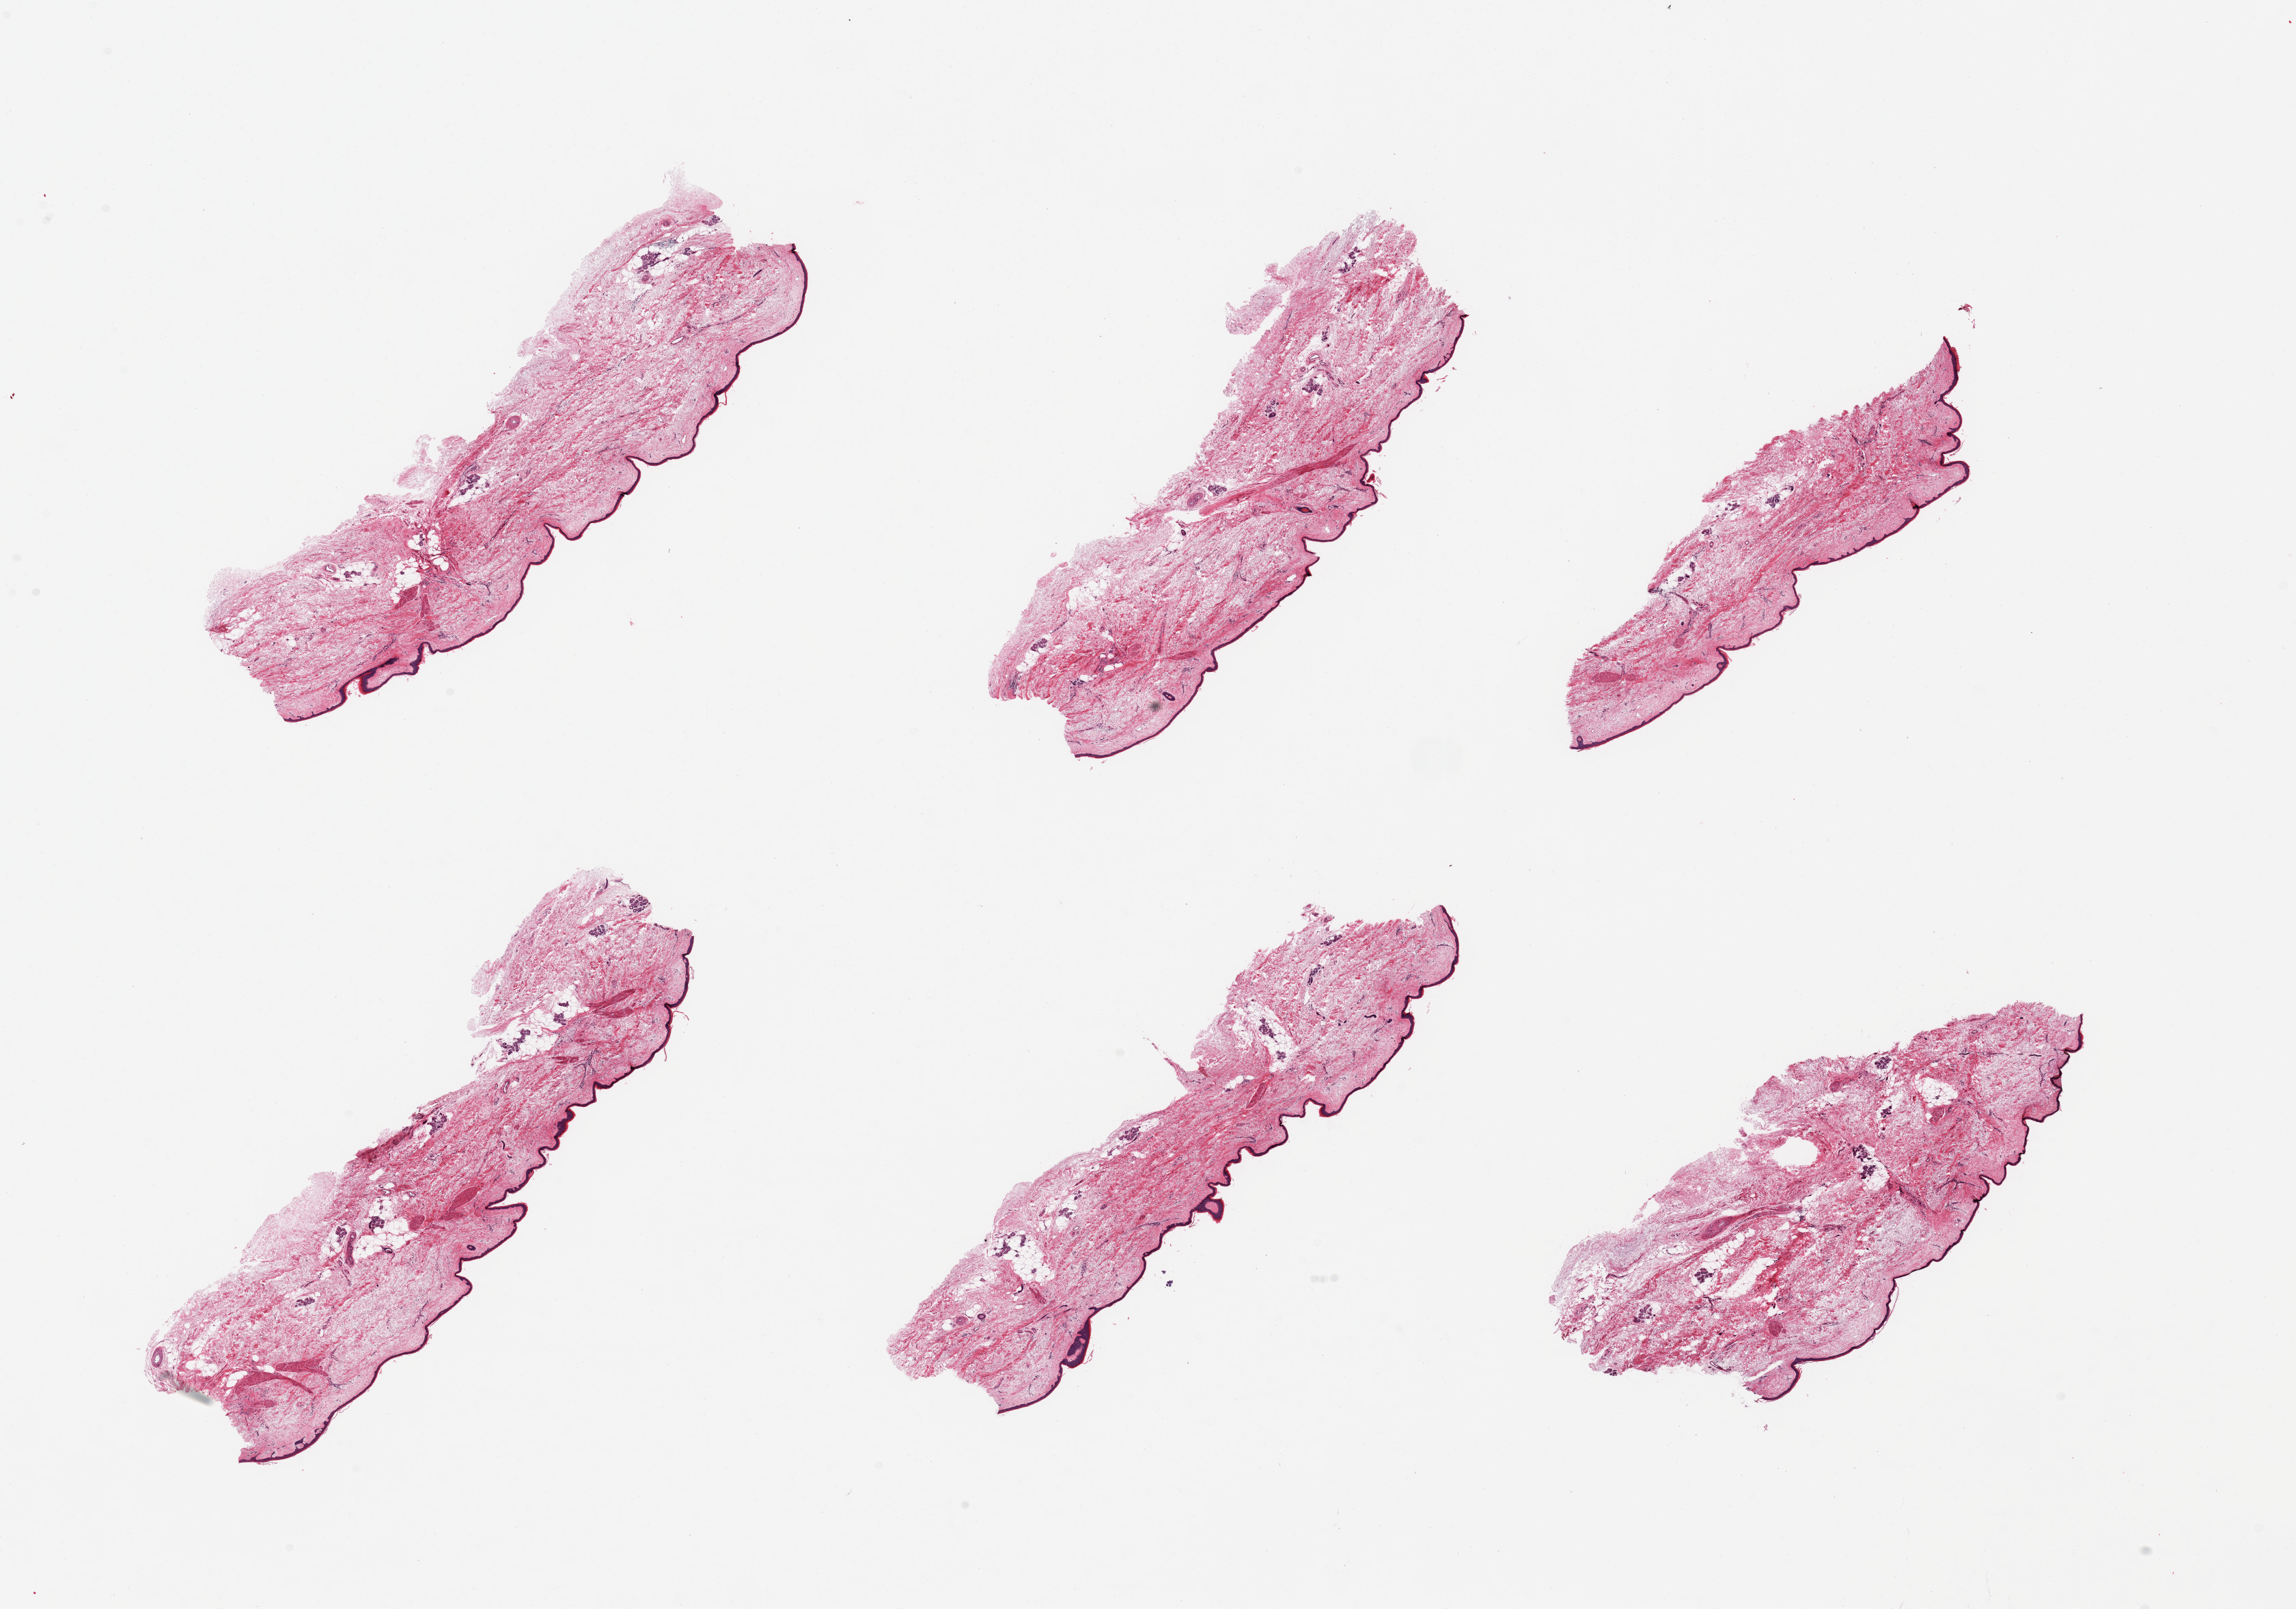
Whole-slide image, haematoxylin and eosin stain, brightfield, a low-resolution overview of the entire scanned area, about 26.6 x 18.6 mm (acquisition: 20x scan); PAXgene-fixed, paraffin-embedded tissue; section of skin of lower leg (target tissue); tissue donor sample. Donor: female.
Reviewer comment on this tissue sample: 6 pieces, squamous epithelium is ~35 microns; no dermal fat.